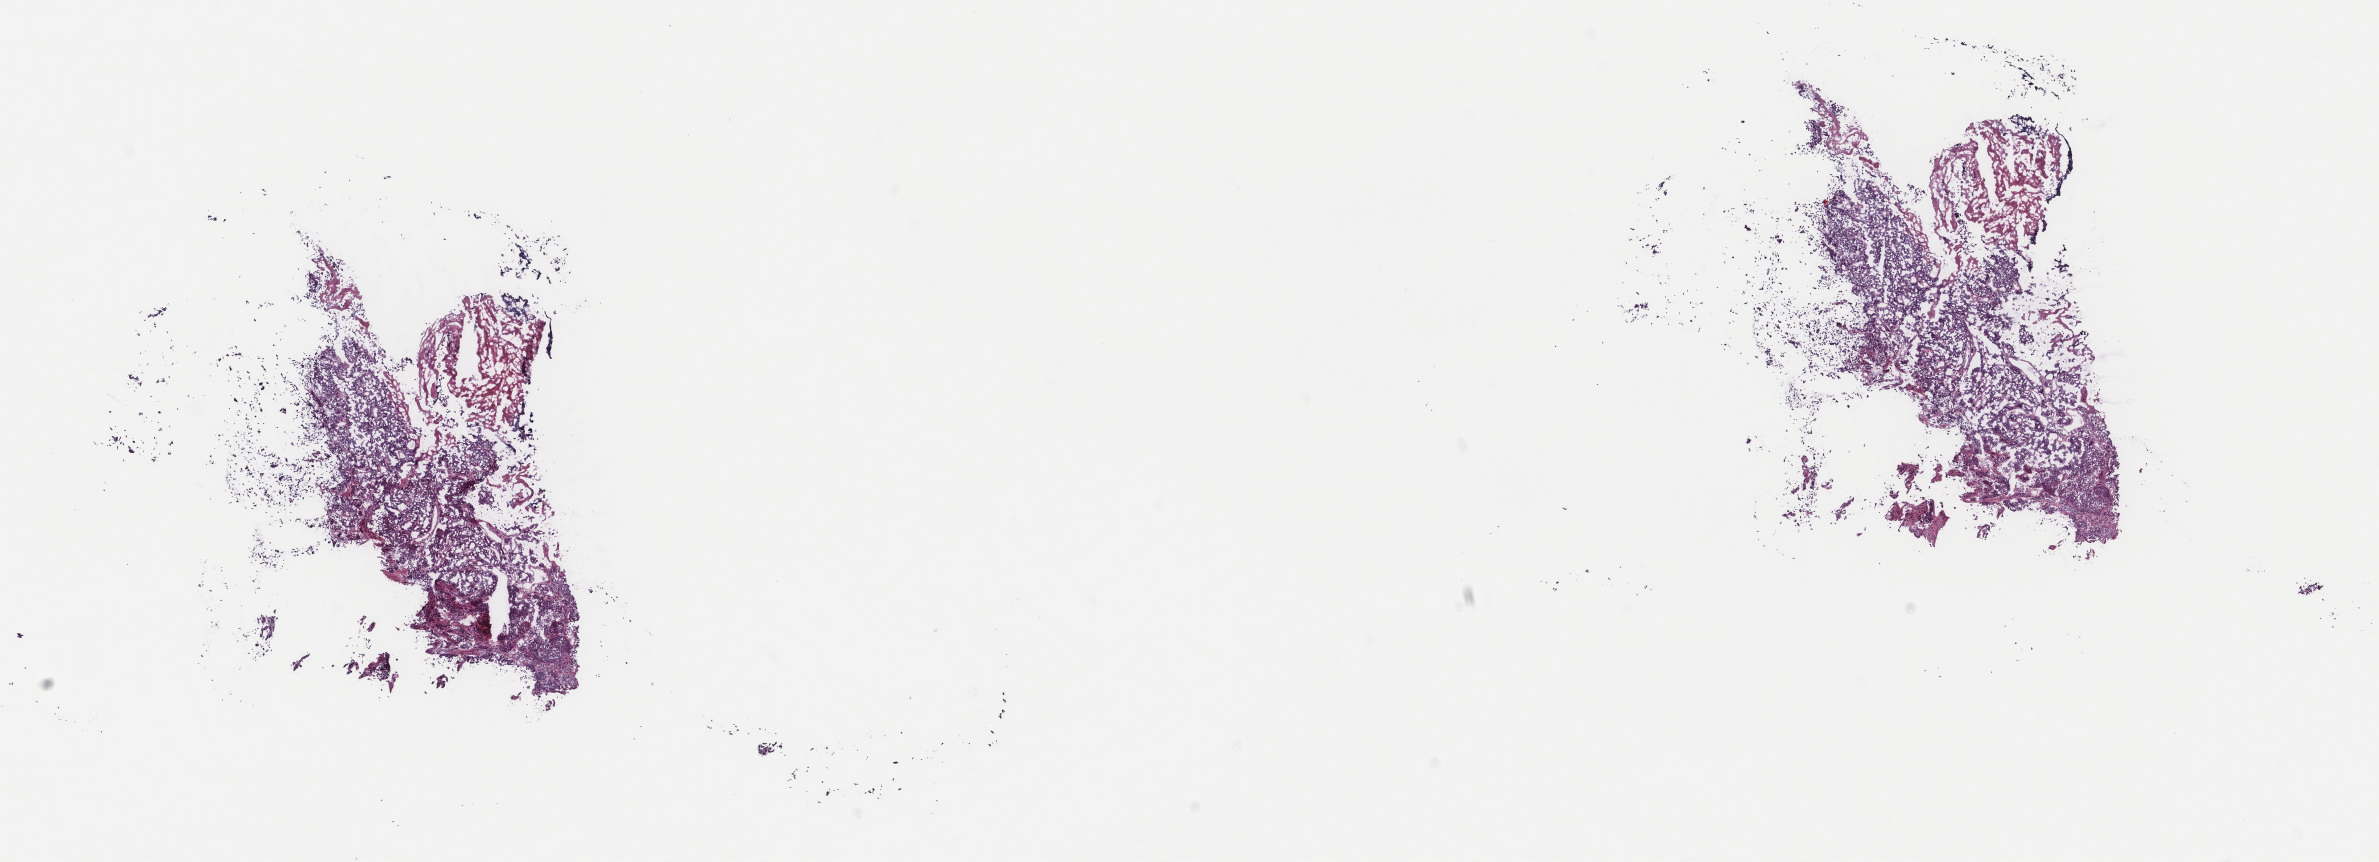
Digitized H&E tissue section (whole slide), low-resolution overview of the scanned area, about 18.9 x 6.8 mm, frozen section from the top of the tissue portion, bladder, primary tumour sample. Male, age 70 years at initial diagnosis. Histologic grade: high grade. Composition of this section per pathologist review: tumour cells 80%, tumour nuclei 80%, normal cells 0%, stromal cells 10%, necrosis 10%. Infiltration values recorded for this section: lymphocyte infiltration 0%, monocyte infiltration 0%, neutrophil infiltration 0%.
* AJCC pathologic stage: II (6th edition)
* pathologic diagnosis: Transitional cell carcinoma (trigone of bladder)